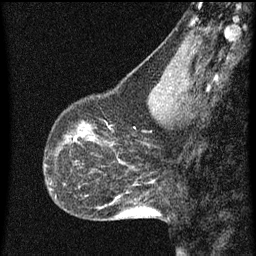
Breast MRI (dynamic contrast-enhanced), one sagittal slice; slice 22 of 60 in the series (ordered by position); dynamic contrast-enhanced series, image 2 of 3 at this slice position (ordered by acquisition); 1.5 T; TE 4.2 ms, TR 8 ms; 2 mm slice thickness; 256 × 256 image matrix, field of view 180 × 180 mm. Patient: female, 43 years.
Annotated regions visible in this slice (semi-automatic segmentation, software-assisted and operator-edited):
- analysis volume of interest (the breast-tissue region the enhancement analysis was run in; not a lesion): bounding box [x1, y1, x2, y2] px = [53, 104, 101, 151]
- tumour enhancement mask (voxels above the 70 % enhancement threshold inside the analysis volume of interest): [68, 132, 83, 143]